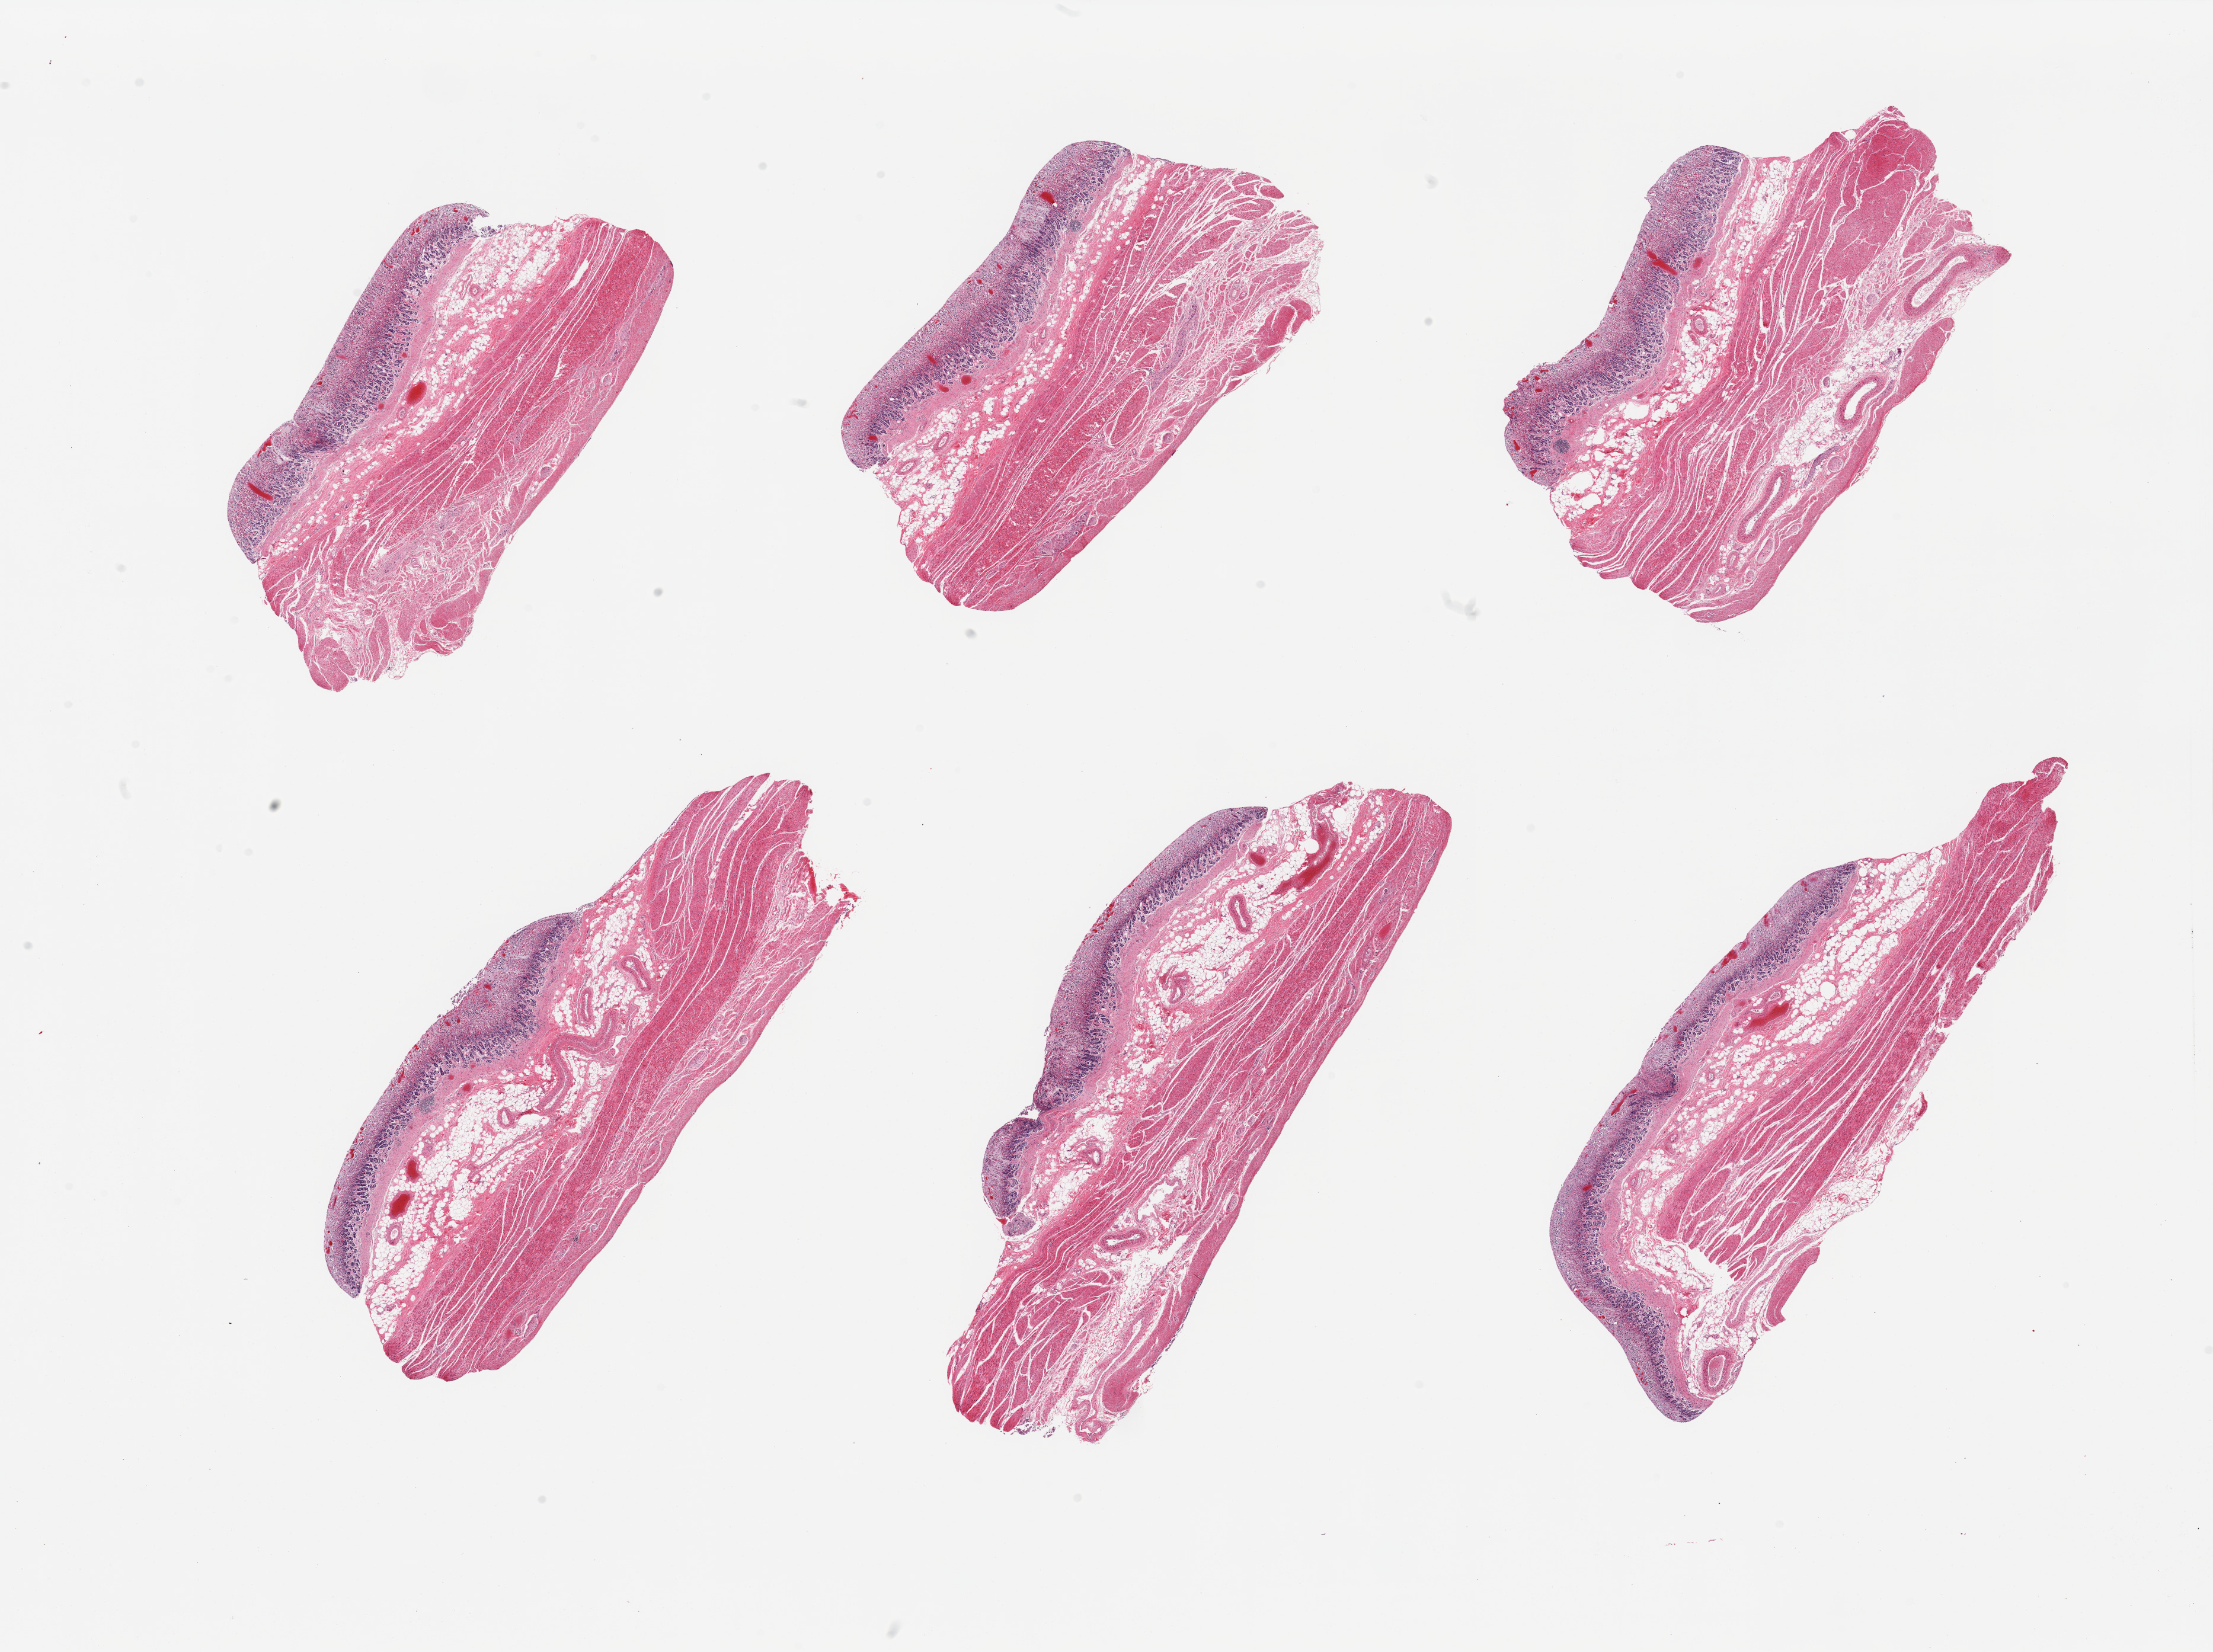
H&E whole-slide image, brightfield — a low-resolution overview of the entire scanned area, about 29.5 x 22.1 mm (from a 20x scan); PAXgene-fixed paraffin-embedded (PFPE) section; sampled site (target tissue): stomach; donor tissue sample. Male donor.
Pathologist's review note for this sample: 6 pieces, mucosa (~0.8mm) up to 20-25% thickness but glandular elements markedly autolyzed except for deeper areas.